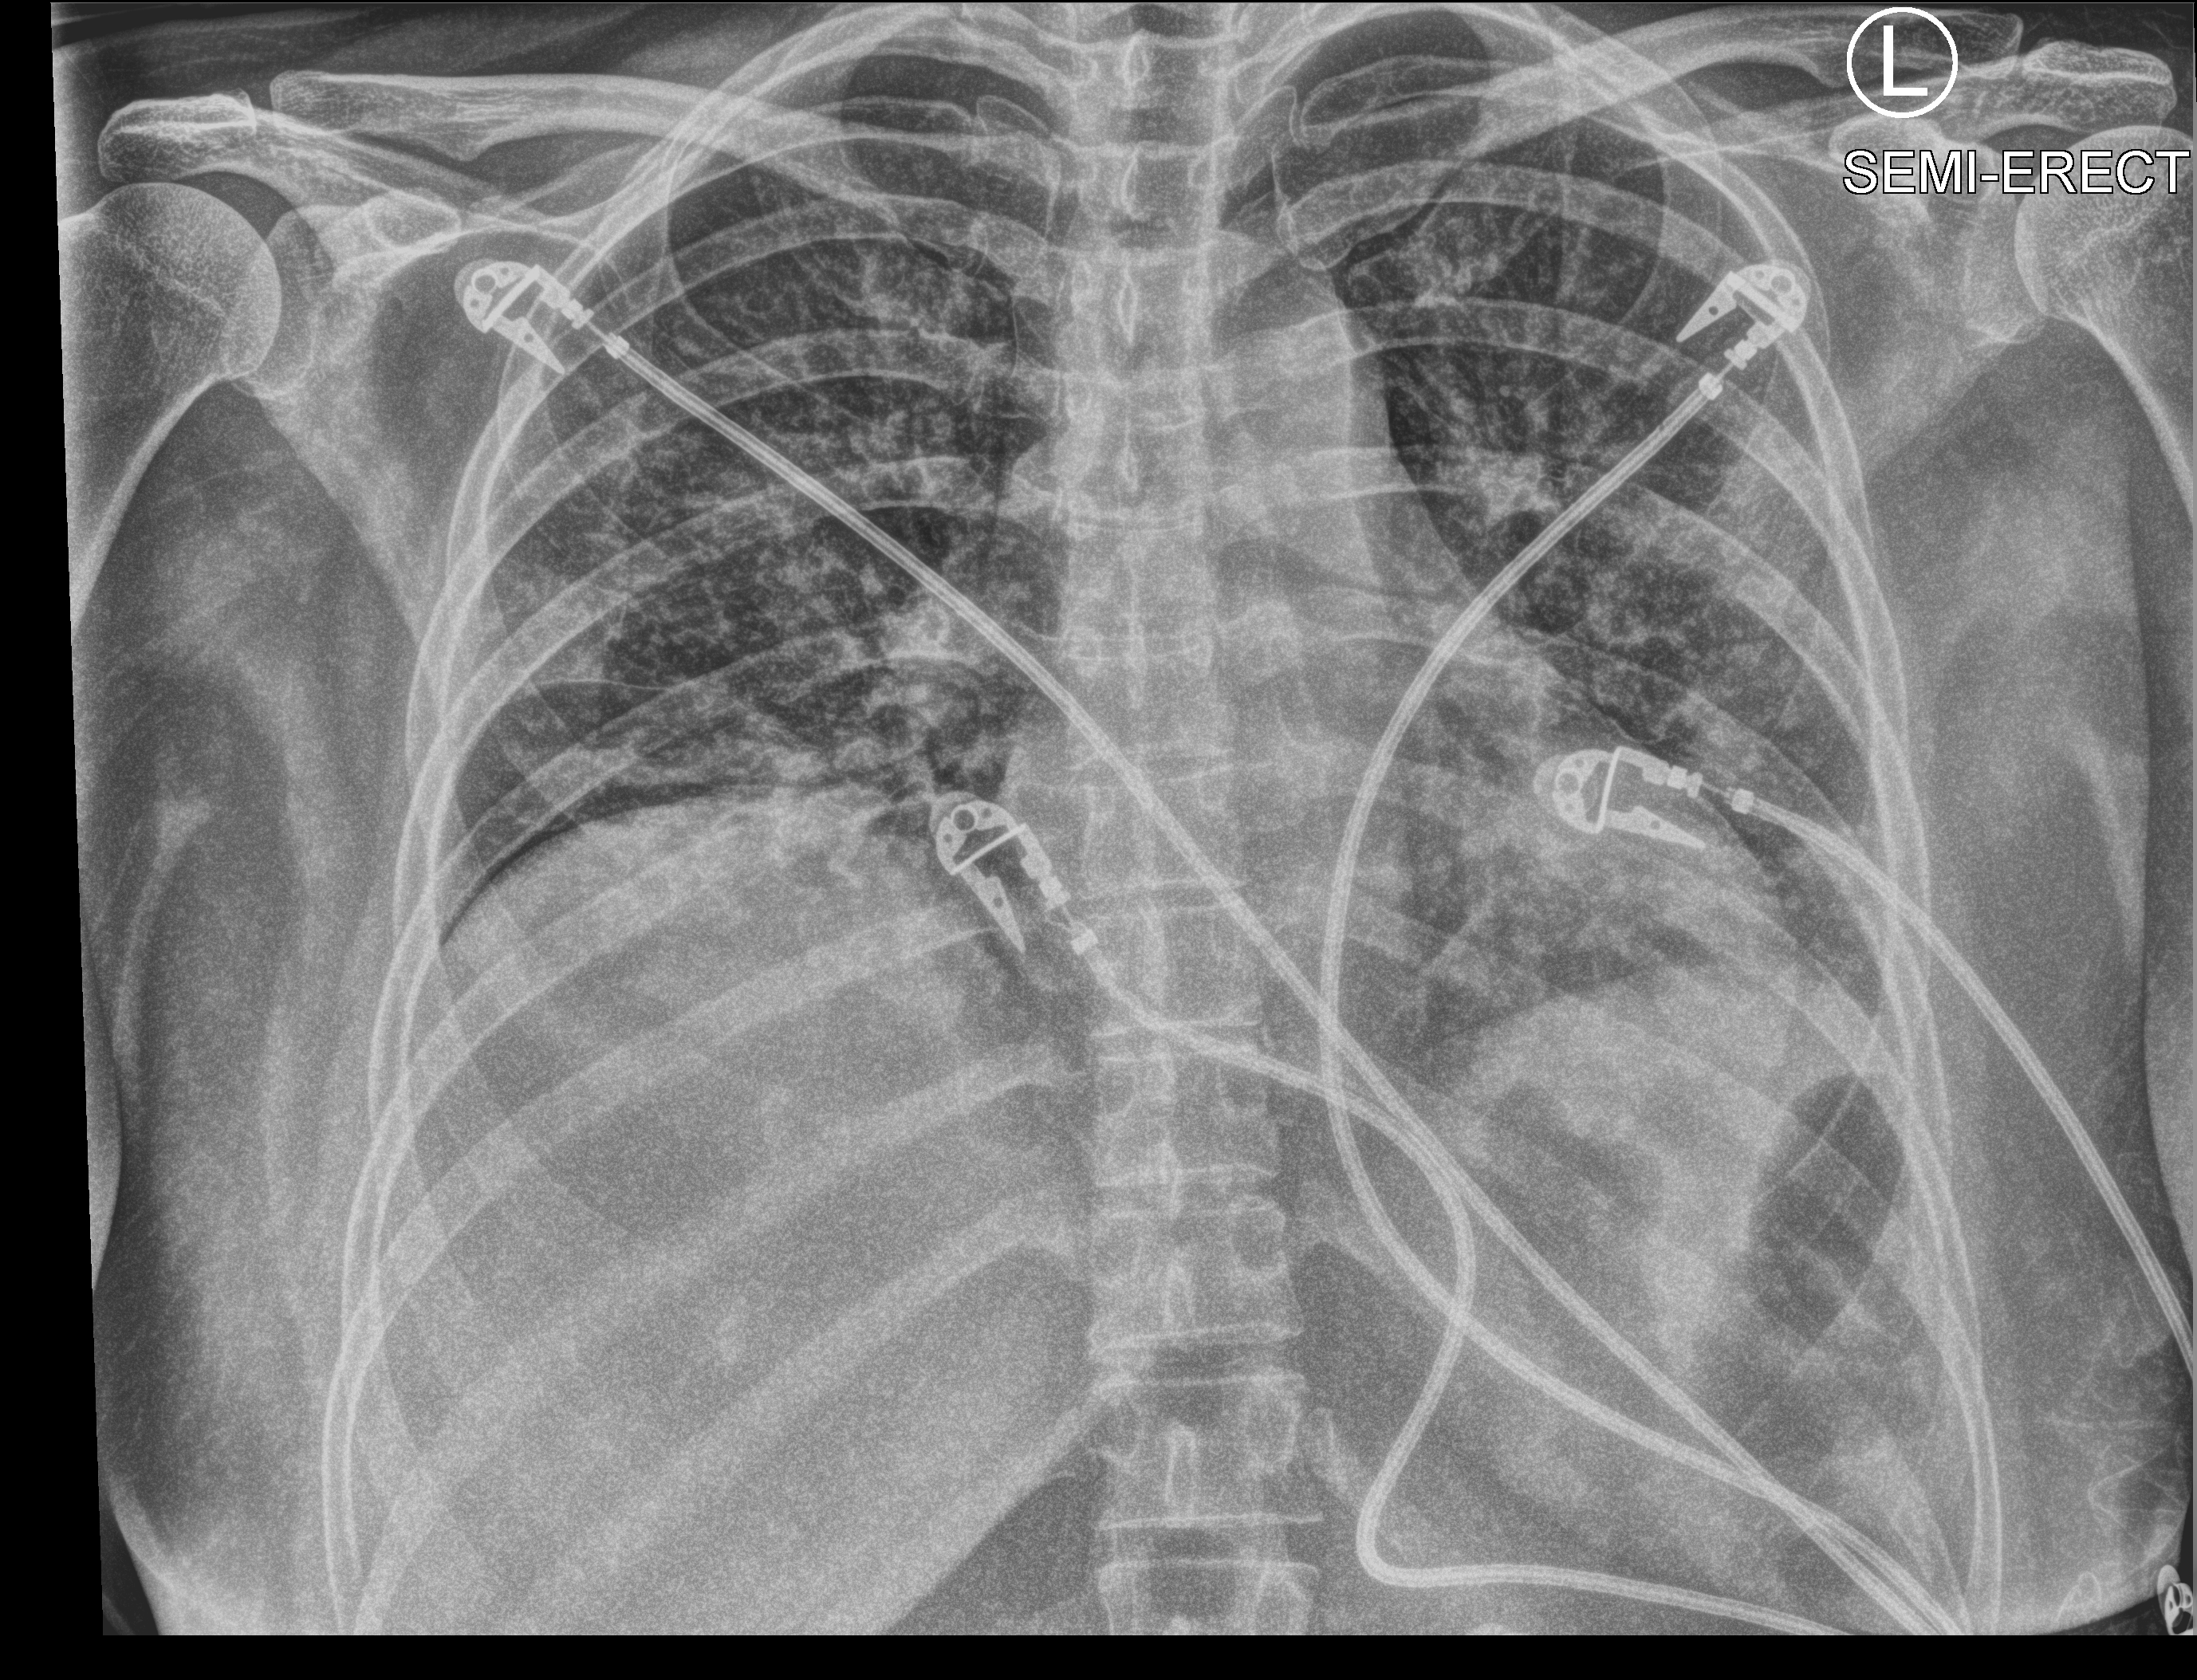
Bedside chest radiograph (computed radiography). Female patient hospitalised with COVID-19, age 18–59 years.
Admission-level facts for this patient (not findings on this image; timing relative to this image not recorded):
- admitted to intensive care during this hospital stay: yes
- smoking status (admission record): never